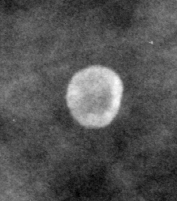
Region of interest cut from a scanned film mammogram (one marked finding); left breast; CC view.
Finding: calcifications, morphology round and regular / eggshell; BI-RADS assessment category 2; benign; no additional work-up was recommended (benign without callback).